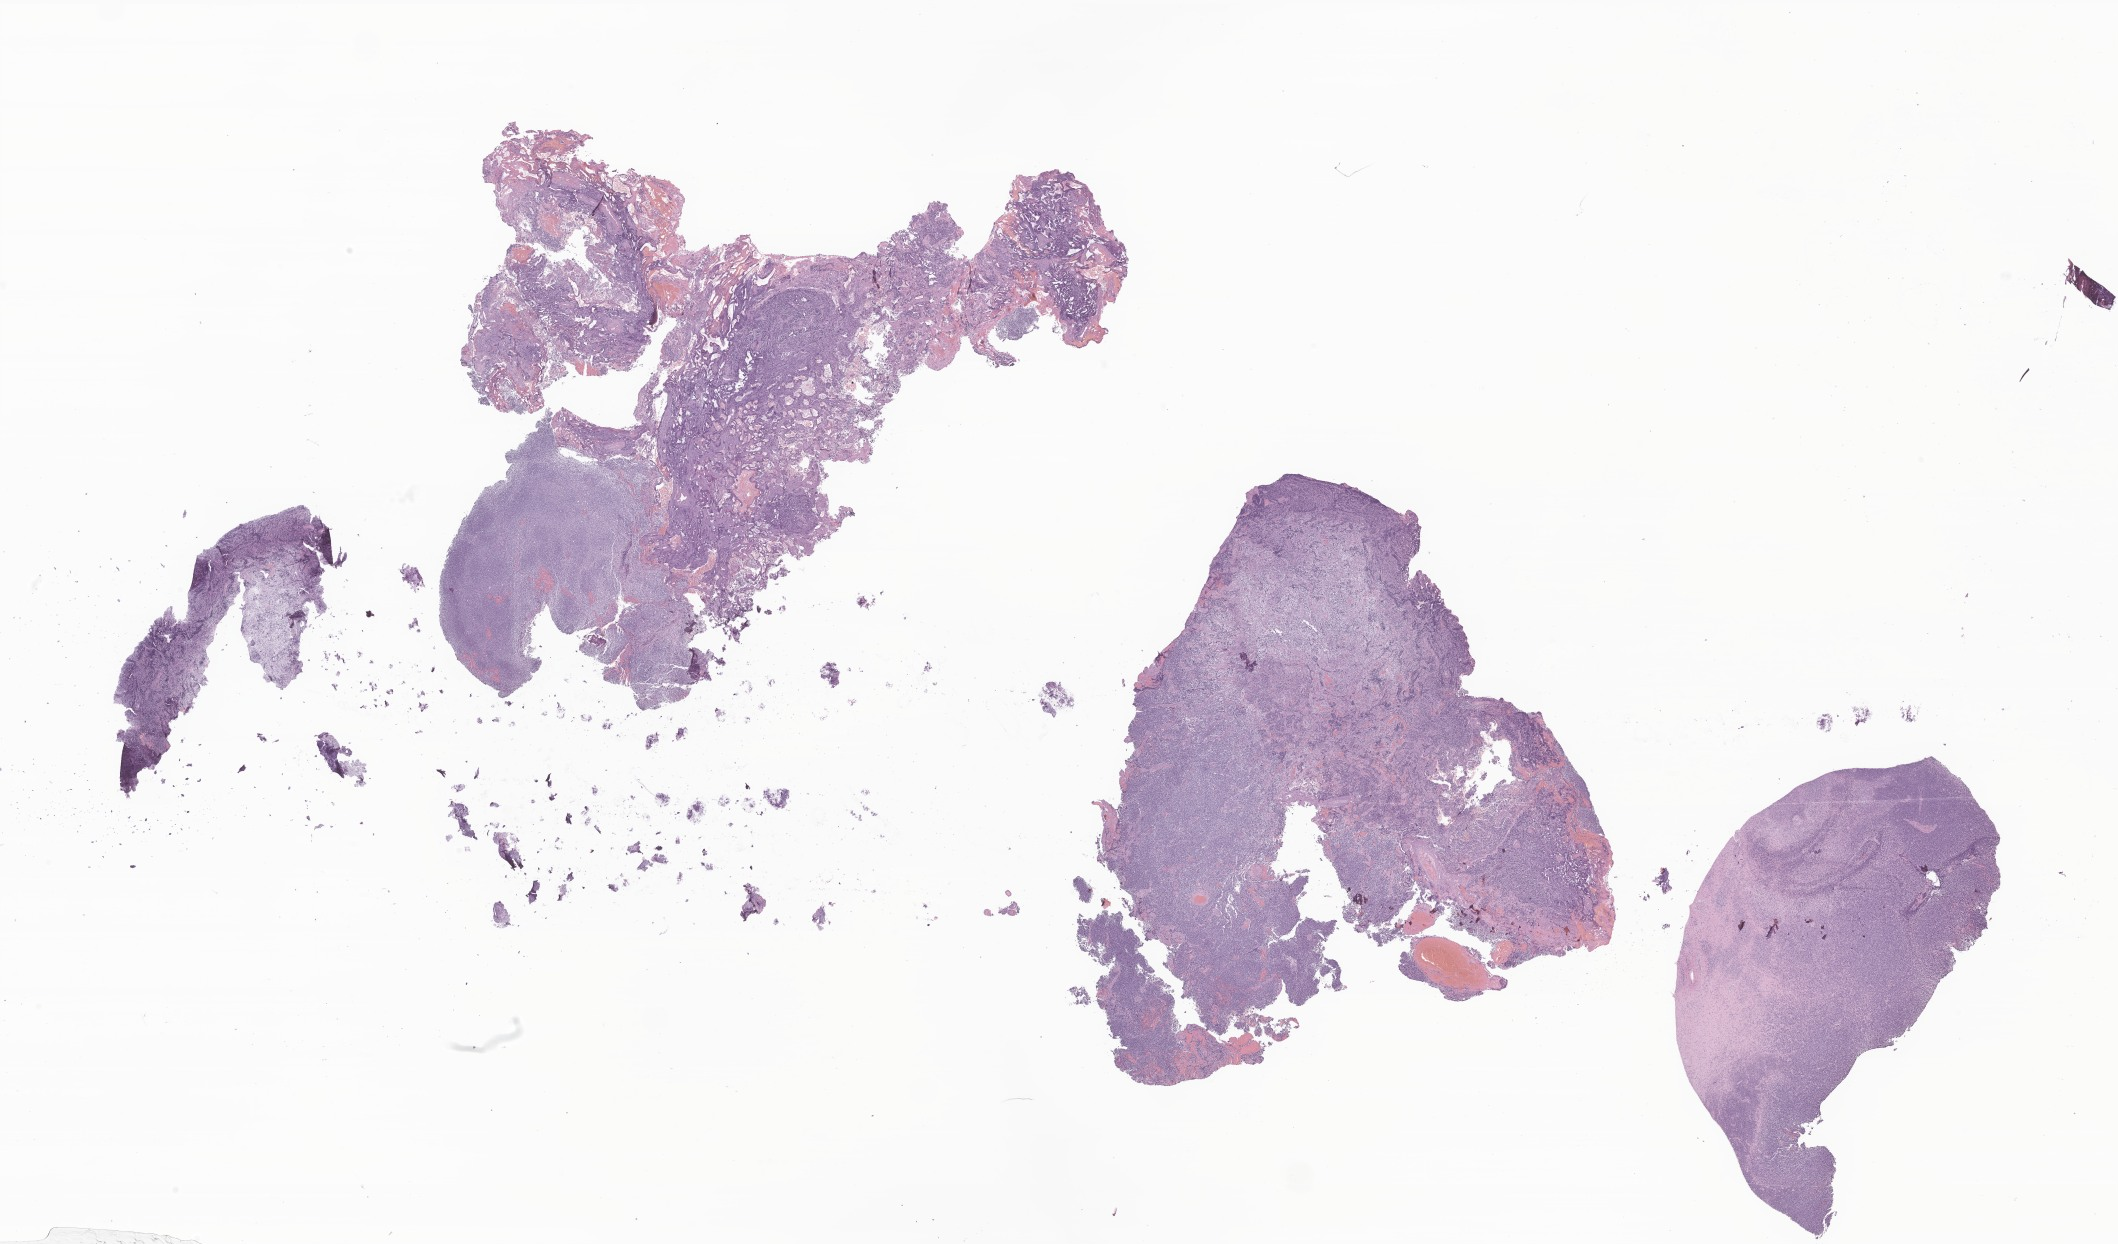
Haematoxylin and eosin whole-slide image of tumor tissue from the cerebellum — whole scanned area (about 35.7 x 21.0 mm) shown as a low-resolution overview; formalin-fixed paraffin-embedded section. Patient: male, age 109 months (9 years 1 month).
• diagnosis (ICD-O-3 morphology term): Medulloblastoma, NOS